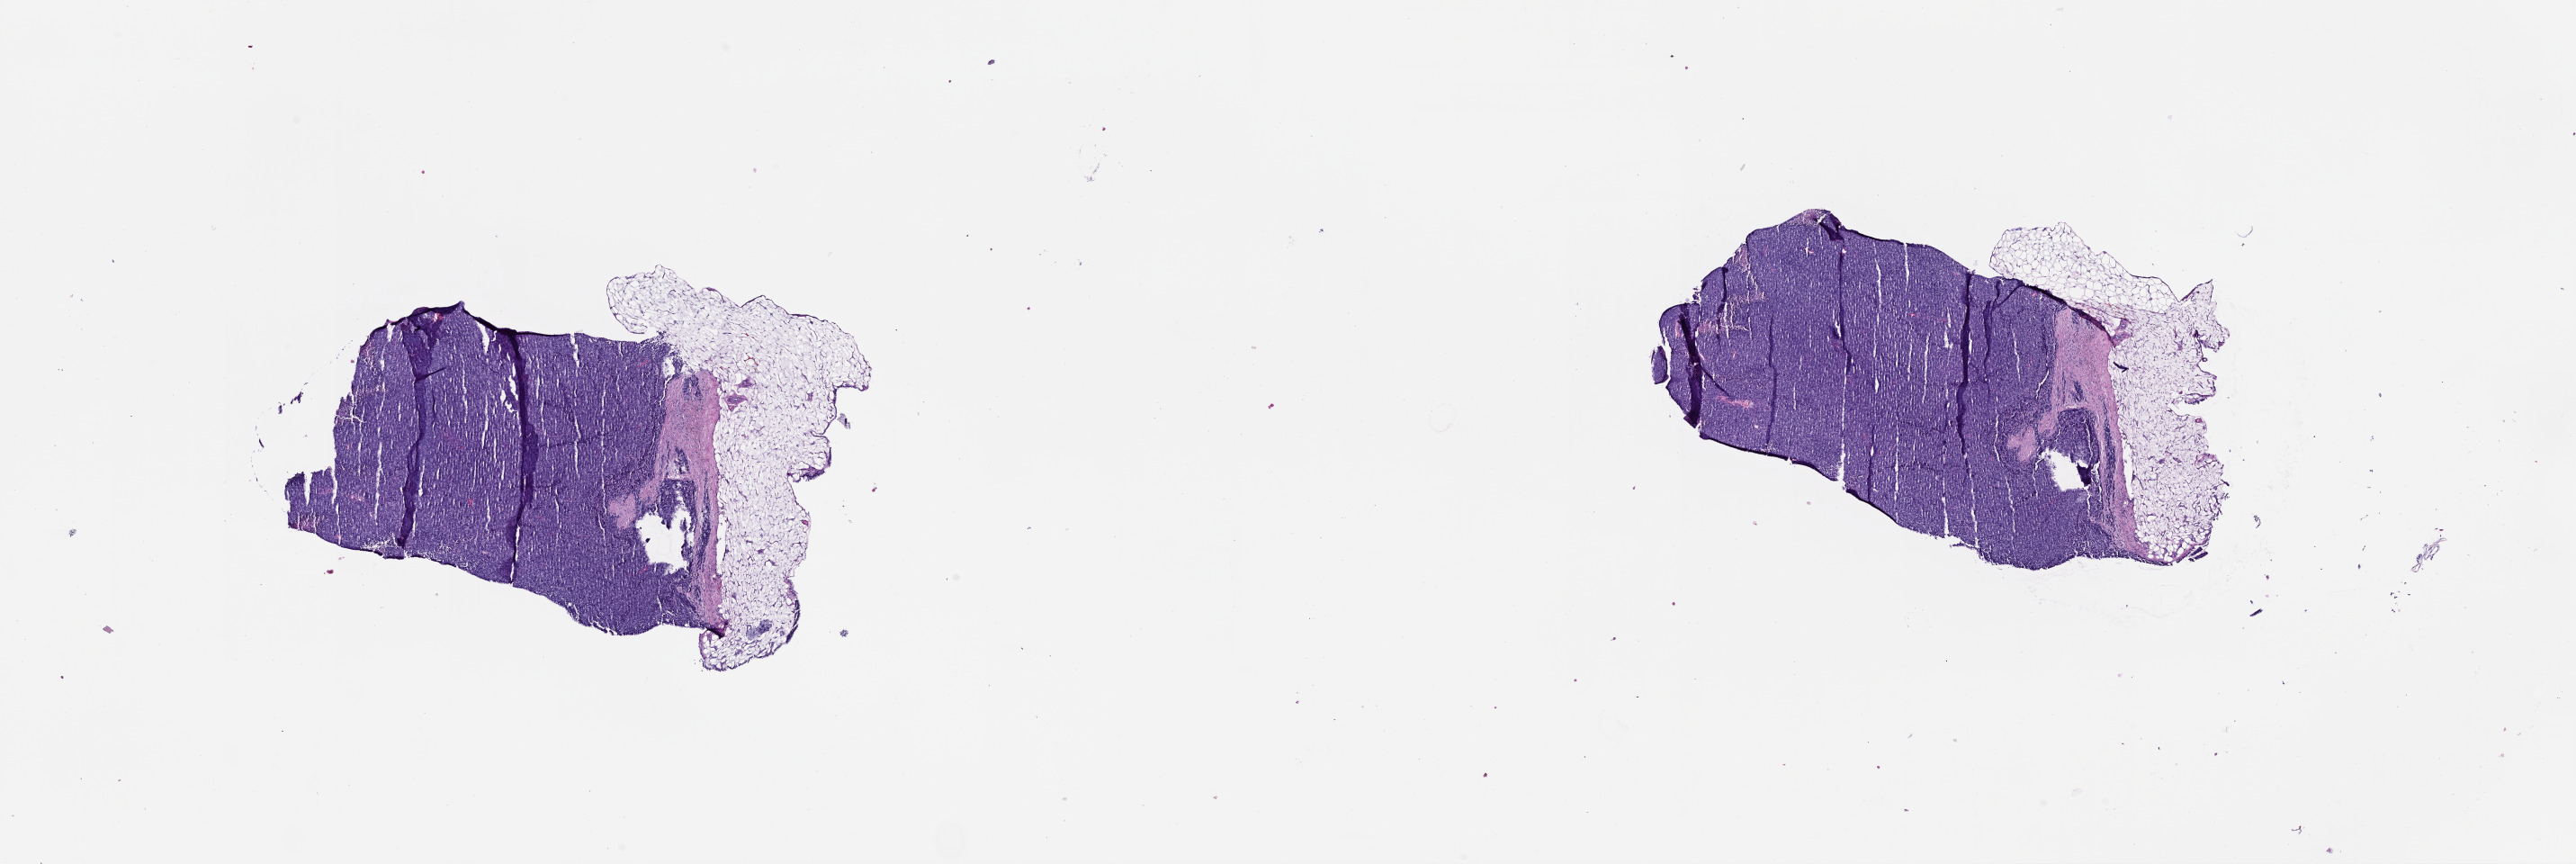
Whole-slide histology image, H&E-stained, shown as a low-resolution overview of the whole scanned area (about 23.1 x 7.7 mm). Tumour tissue sample, sampled site: lymph node. Patient: male, age 53 years. Slide review estimates, as recorded: tumour nuclei 80%, necrosis 0%.
This section: metastatic tumour tissue. Patient diagnosis: Malignant melanoma, NOS.